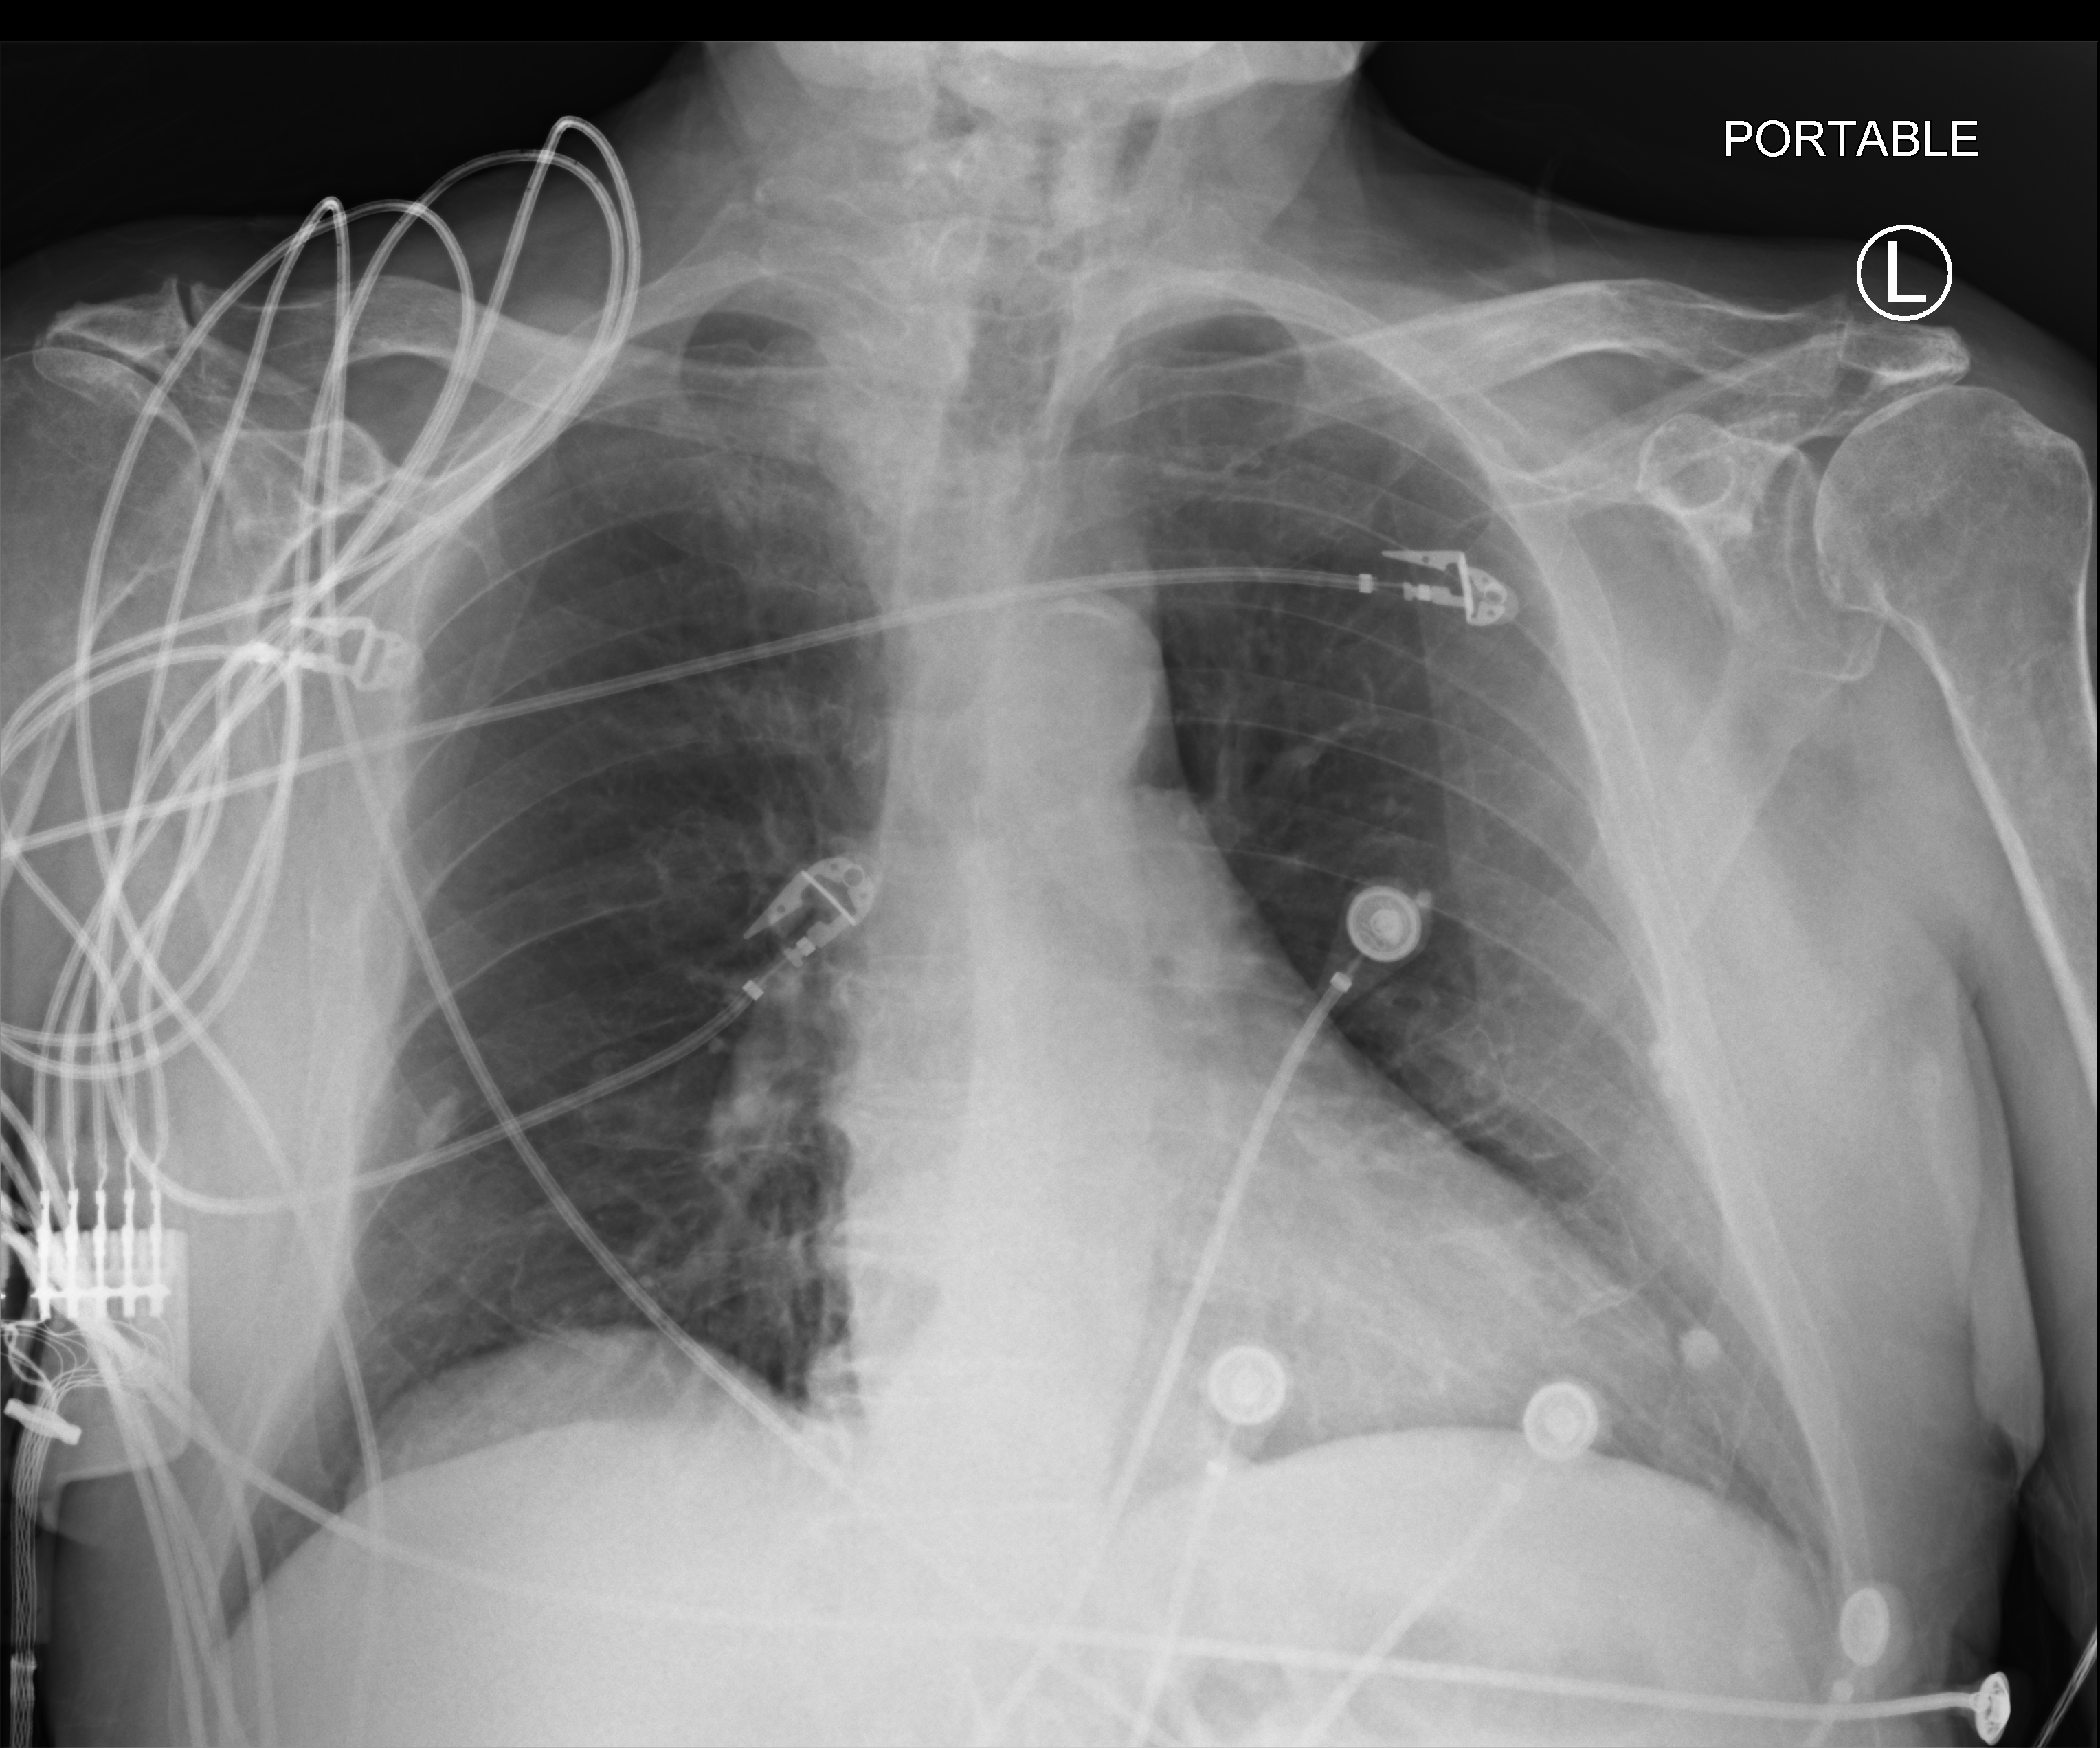
Bedside chest radiograph (computed radiography), anteroposterior (AP) projection. Patient hospitalised with COVID-19; male, aged 75–90 years.
From the hospital-stay record, not from the radiograph (when in the stay this image was taken is not recorded):
- length of hospital stay: 9 days
- admitted to intensive care during this hospital stay: no